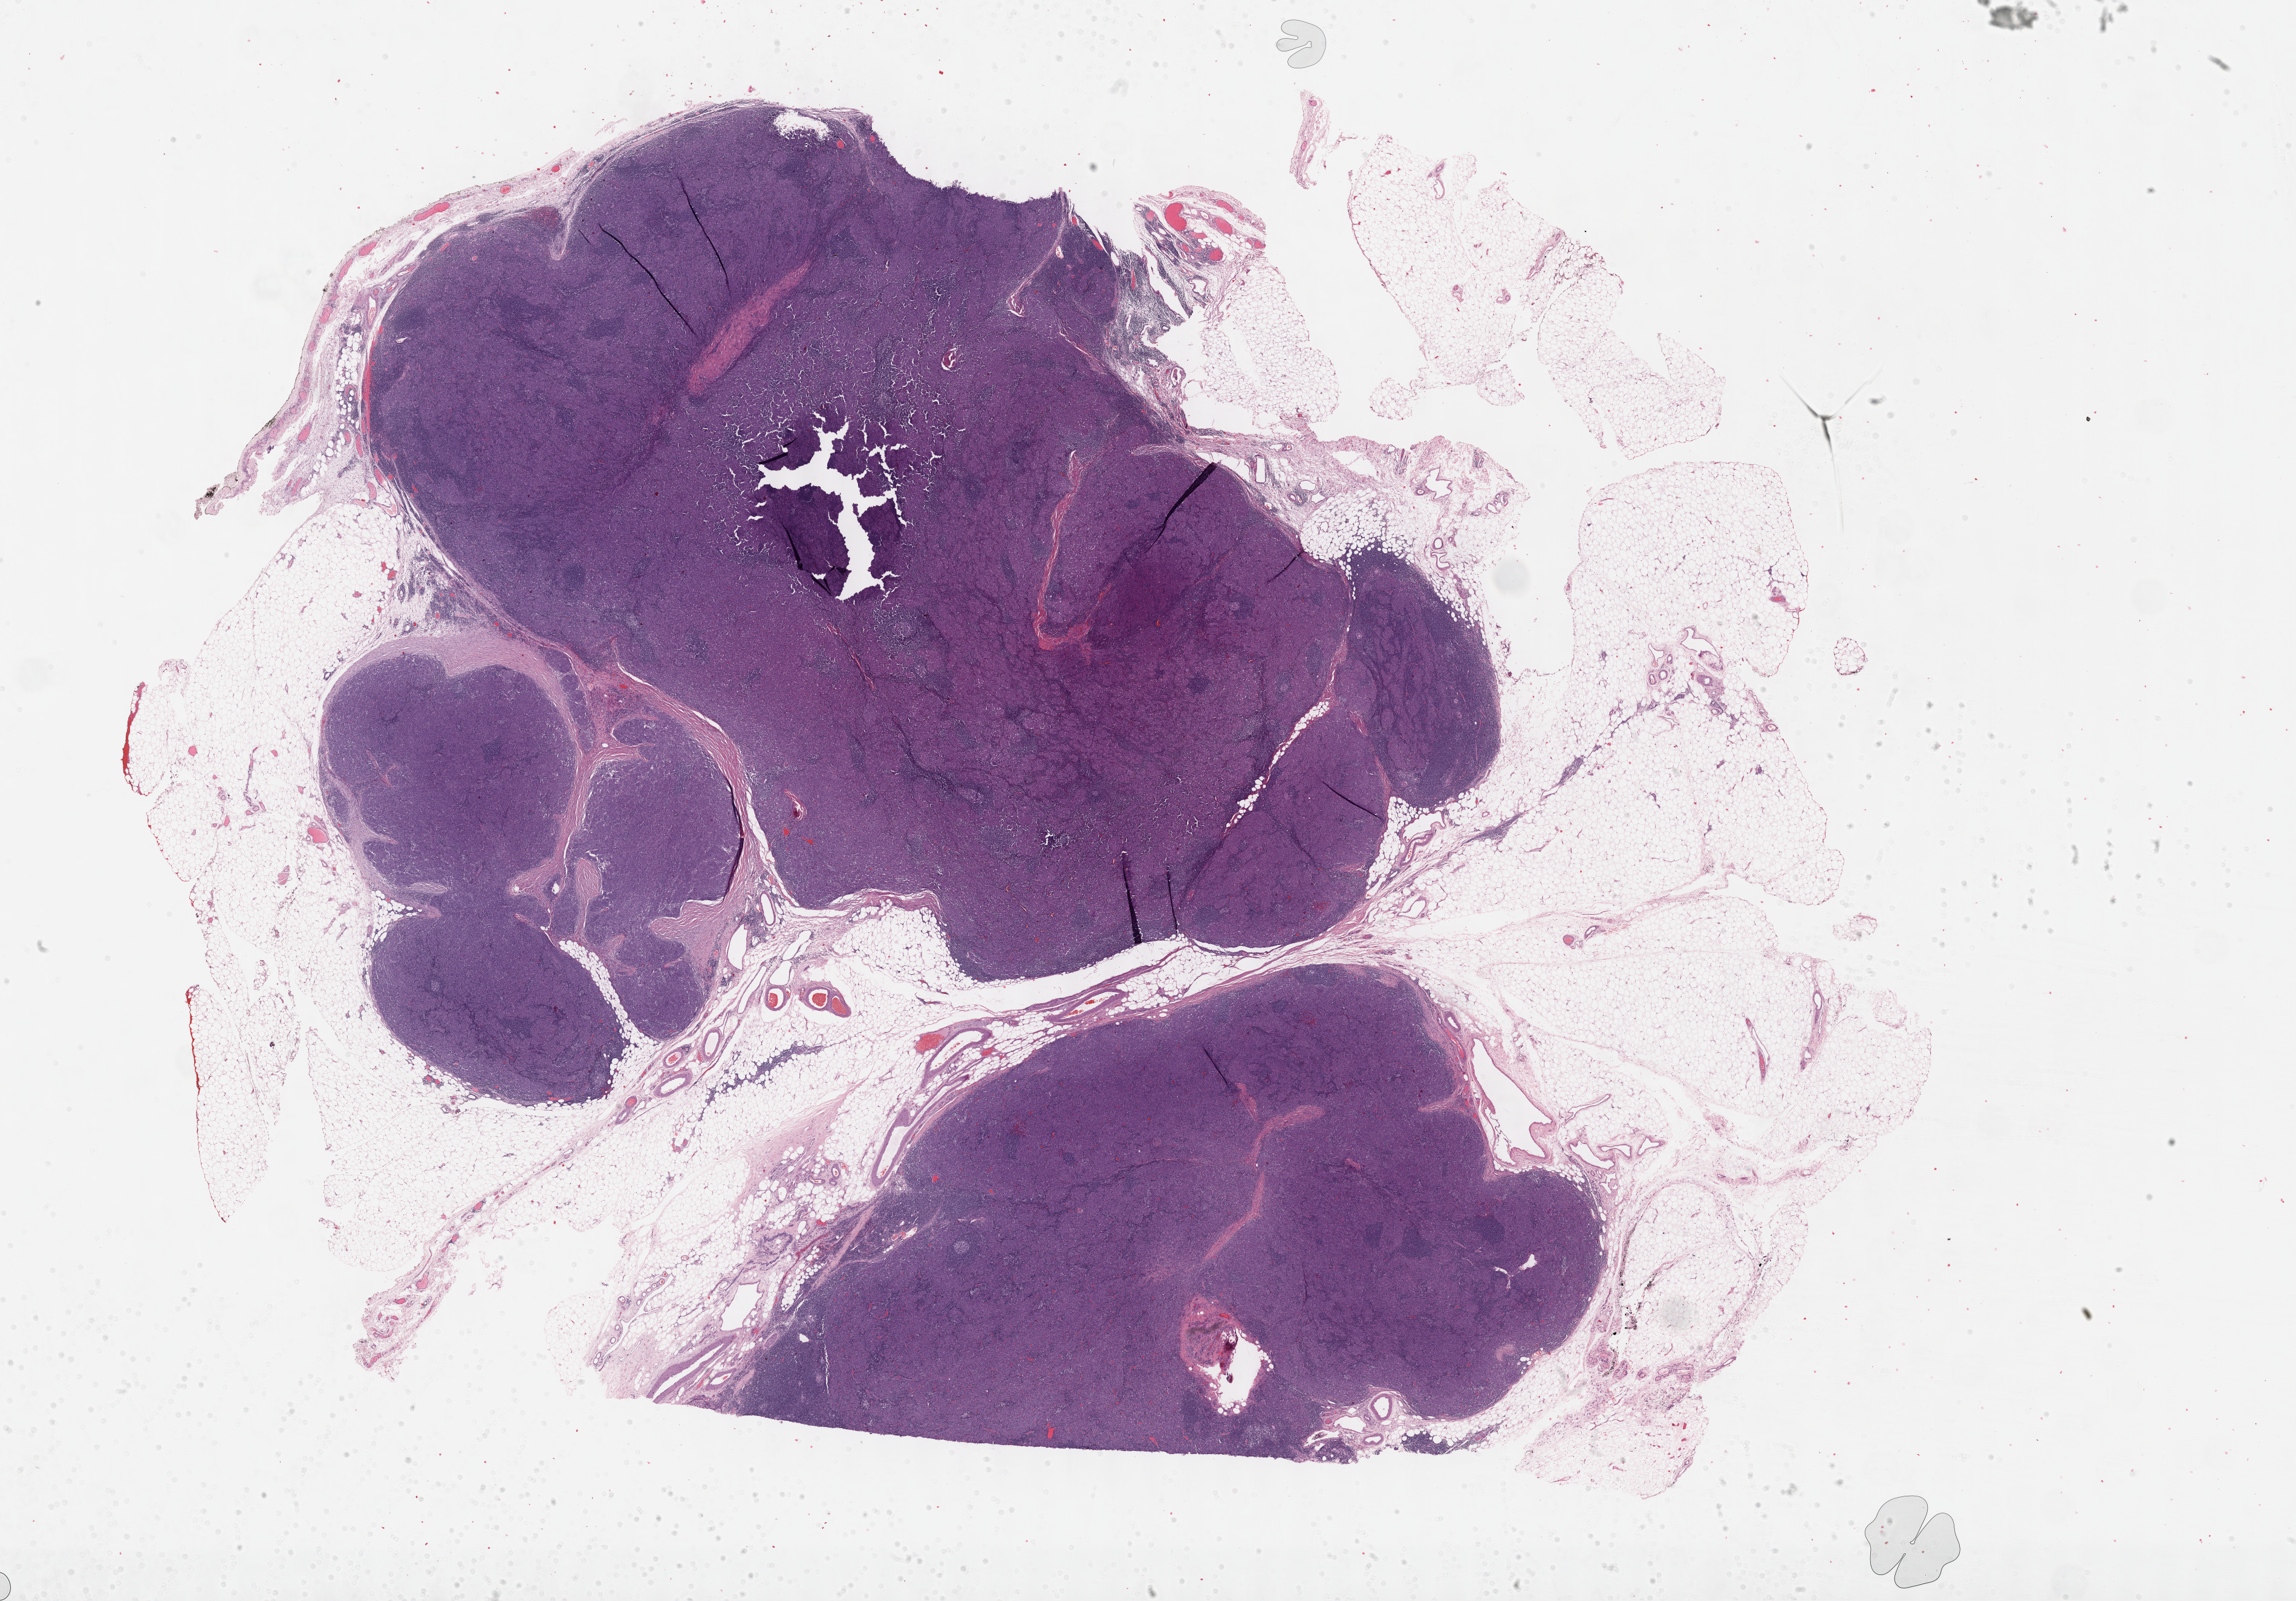
H&E-stained whole-slide image, a low-resolution overview of the entire scanned area, about 30.7 x 21.4 mm (slide scanned at 40x). FFPE section. Sample: primary tumour, thymus. Patient: female, age at initial diagnosis 61 years.
* diagnosis: Thymoma, type B3, malignant